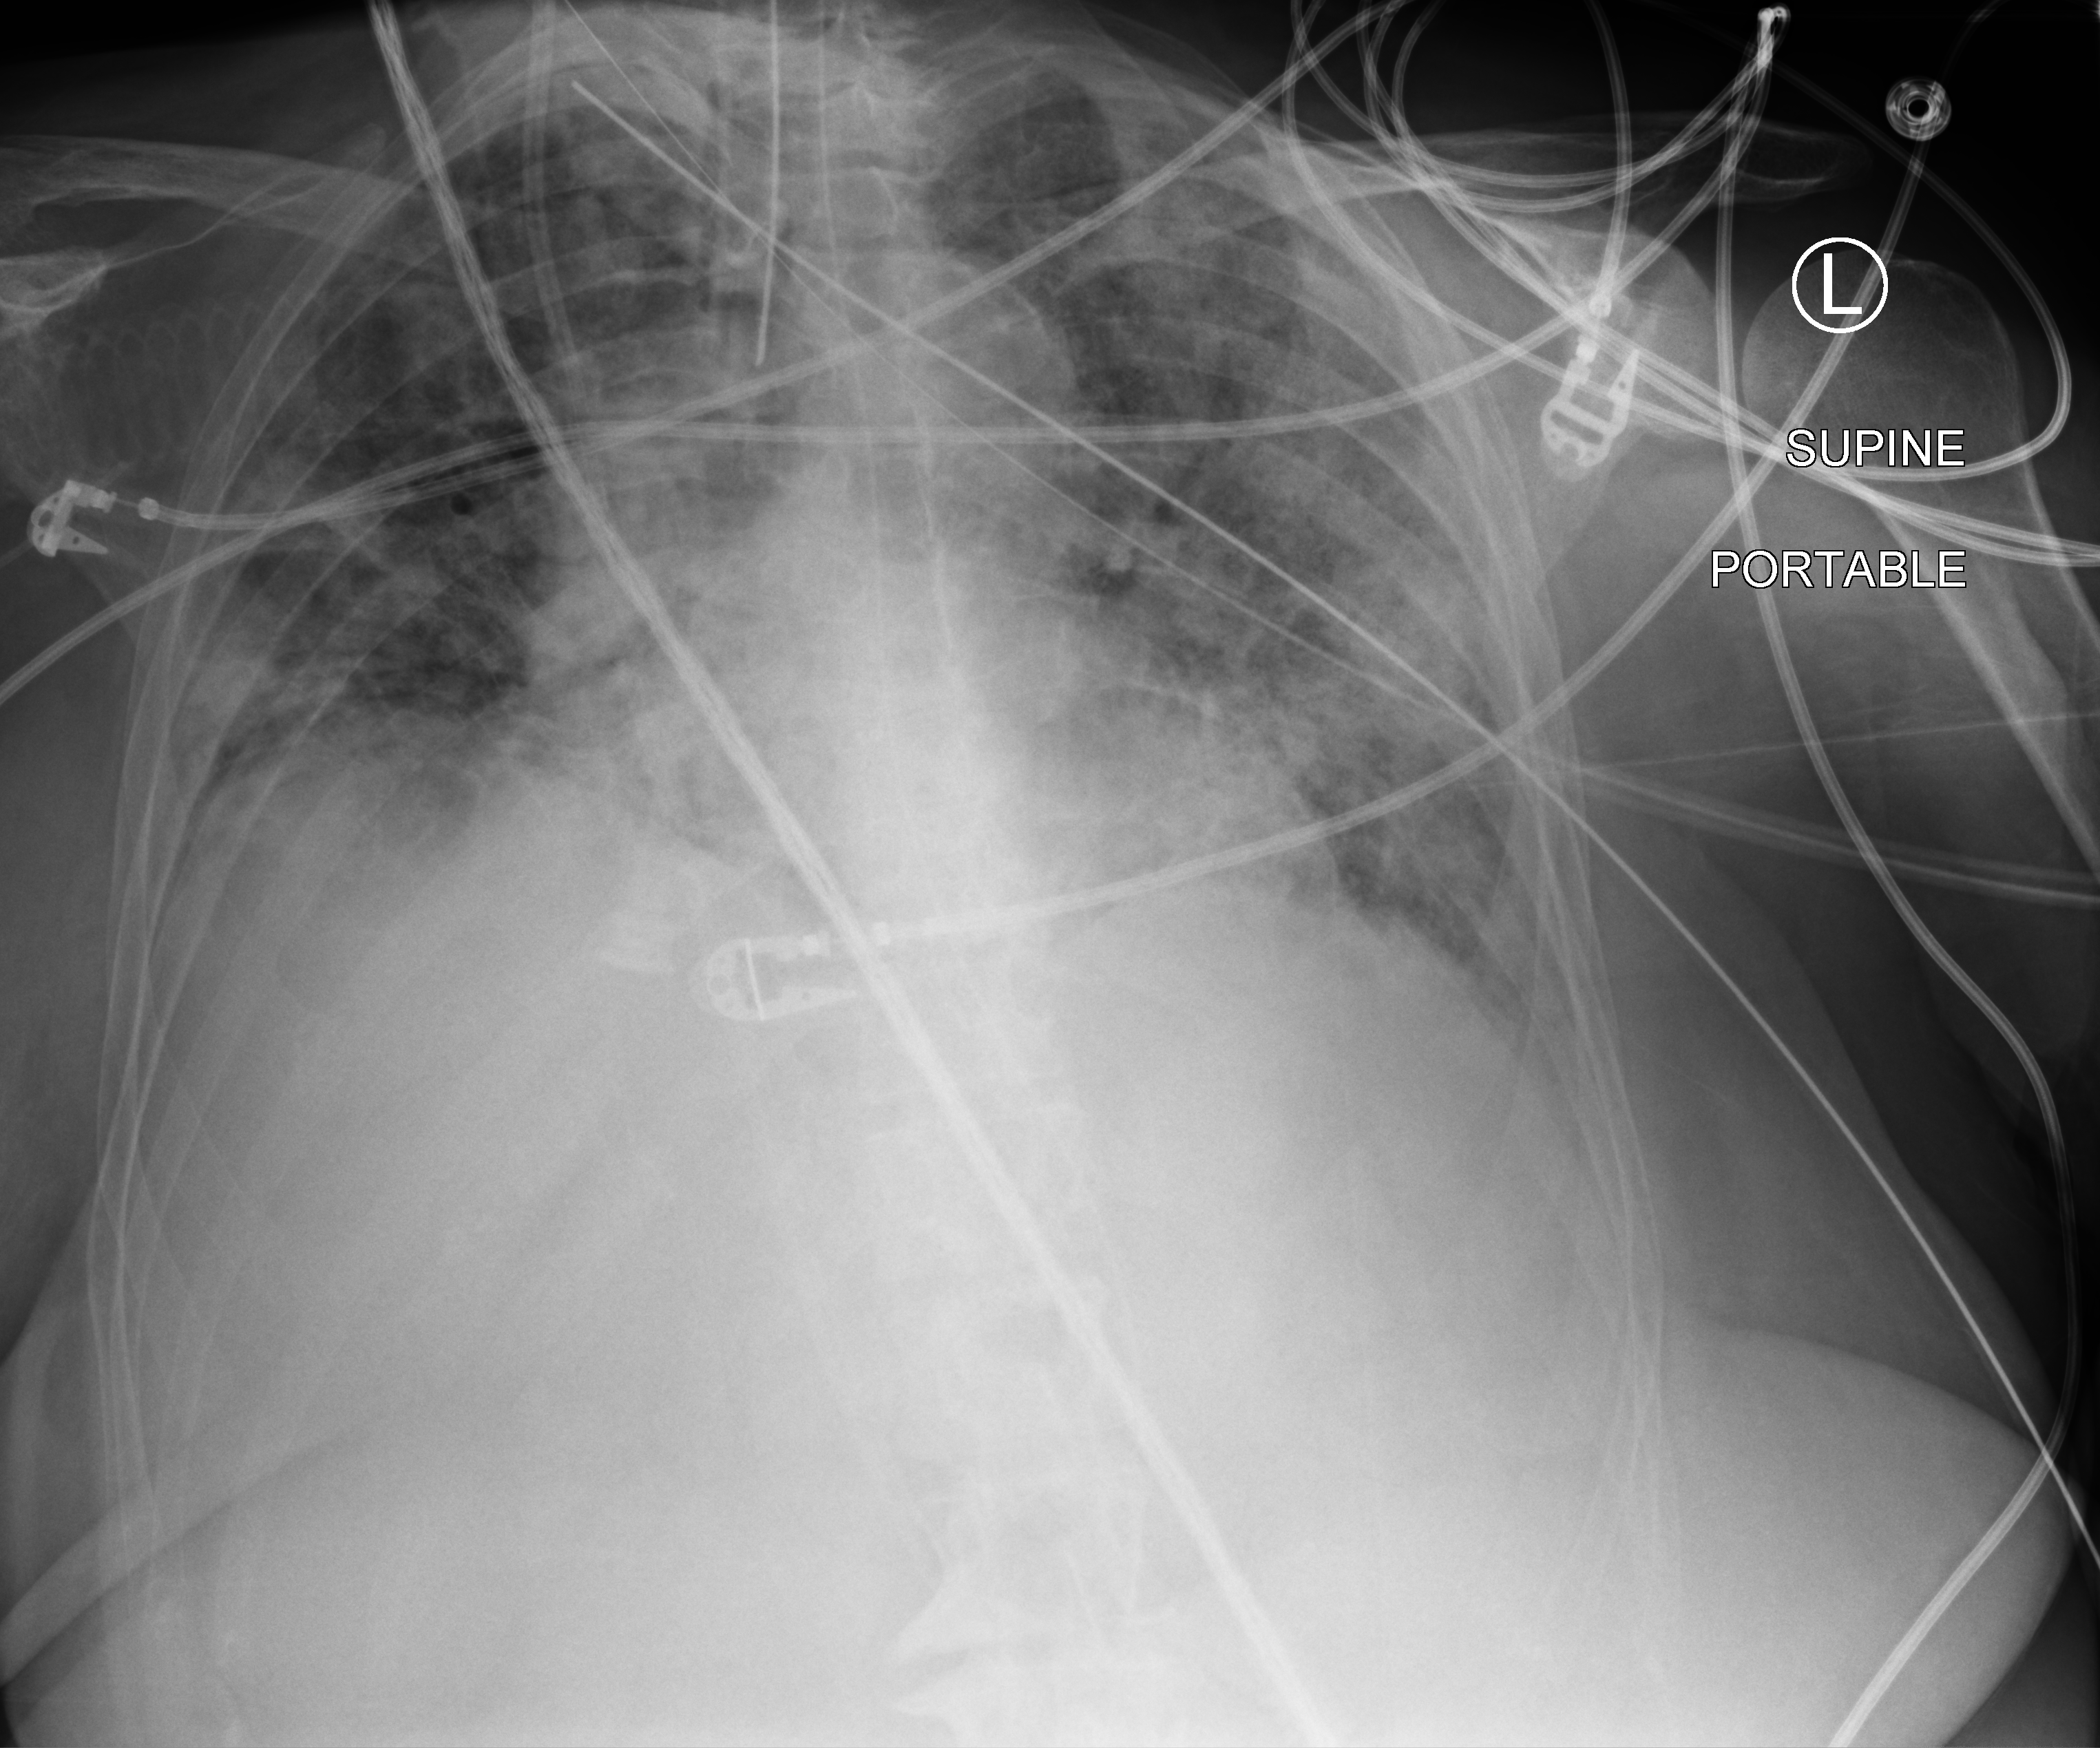
Bedside chest radiograph (computed radiography); anteroposterior (AP) projection. Female patient hospitalised with COVID-19, age 75–90 years.
Admission-level facts for this patient (not findings on this image; timing relative to this image not recorded): admitted to intensive care during this hospital stay: yes; mechanically ventilated during this hospital stay: yes; diabetes (admission record): no.